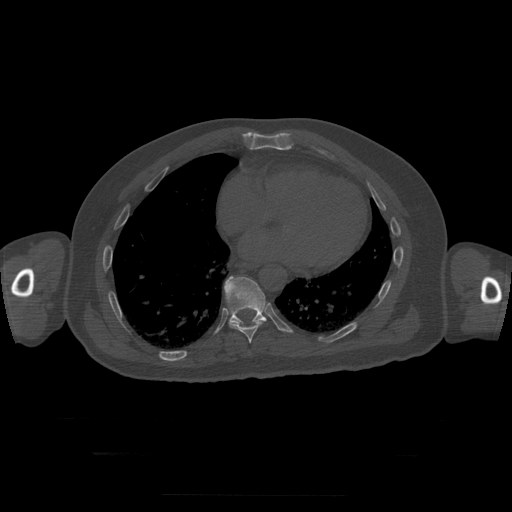
CT including the spine, one axial slice; position 136 of 397 along the scan axis; bone window (W 1800 / L 400 HU); 512 × 512 image matrix, field of view 510 × 510 mm. Patient age 73 years. Case-level facts recorded for this patient, not image findings: primary cancer: prostate.
Outlined on this slice (semi-automatically segmented with operator editing):
- T10 vertebra: bounding box [x1, y1, x2, y2] px = [224, 276, 266, 326]
- T9 vertebra: [229, 319, 266, 344]